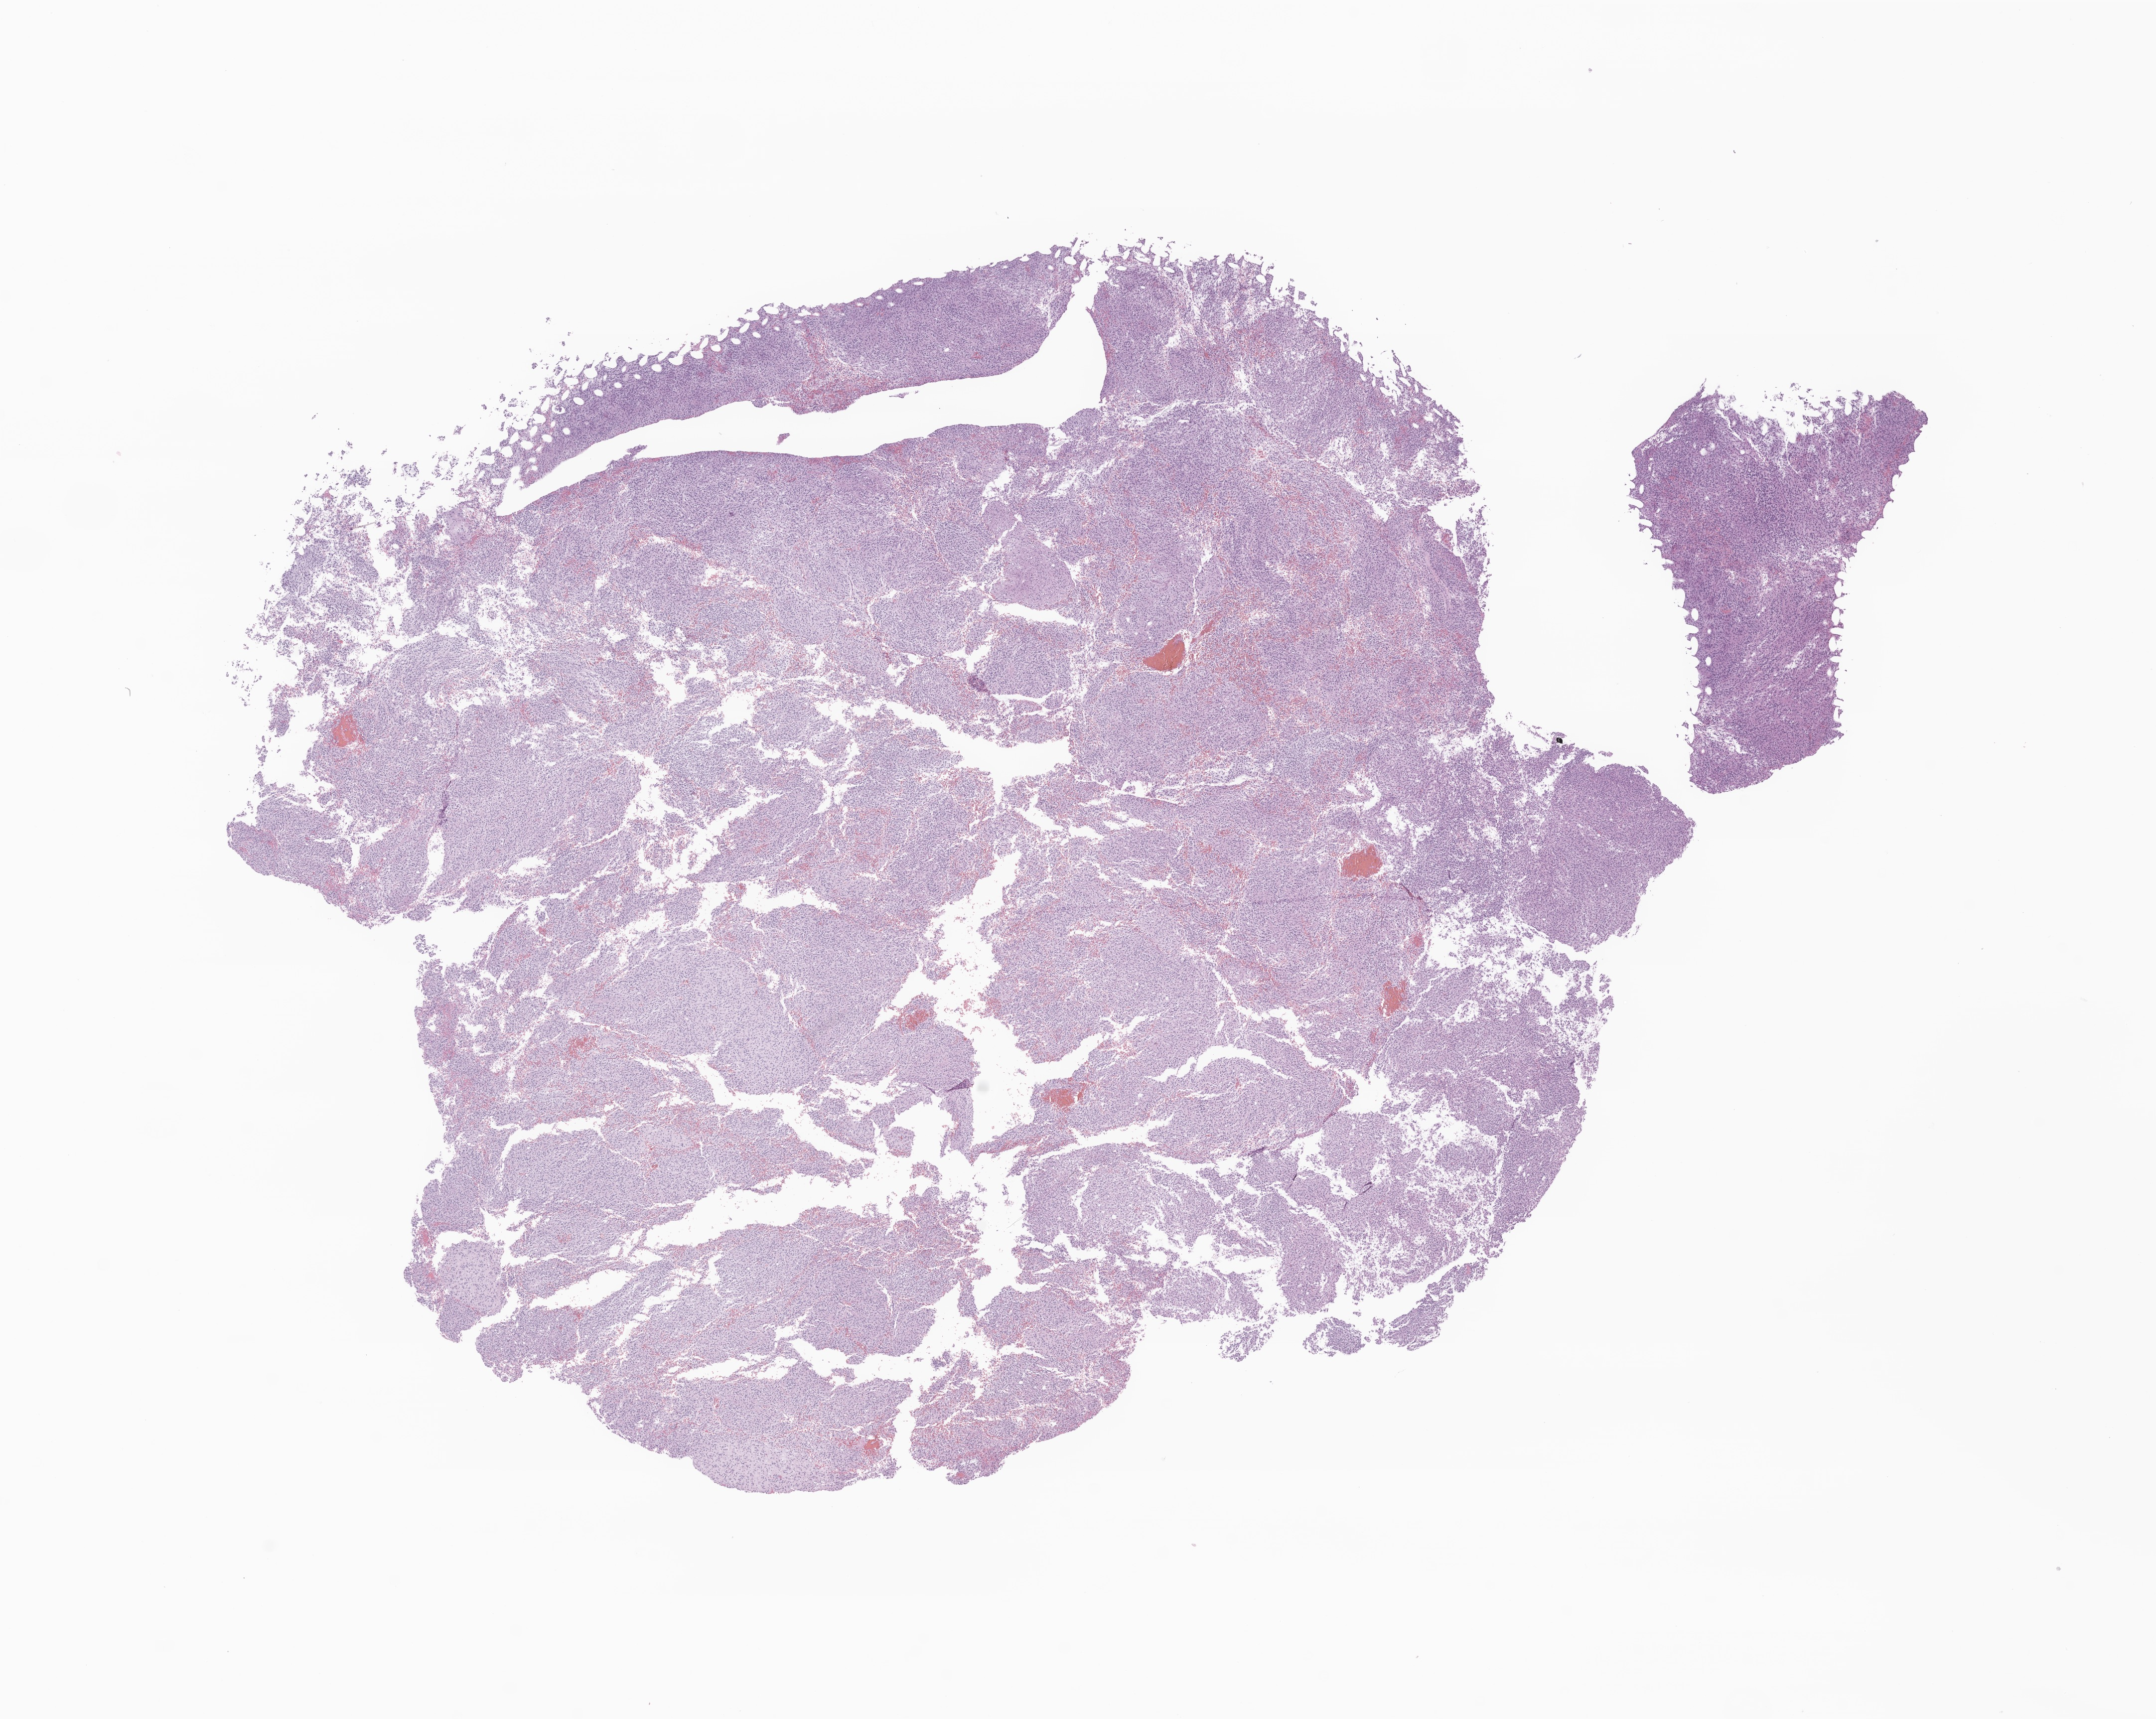
Whole-slide image, hematoxylin and eosin (H&E) stain of tumor tissue from the brain — shown as a low-resolution overview of the whole scanned area (about 18.2 x 14.5 mm), FFPE section. Patient: male, age 124 months (10 years 4 months).
Diagnosis: Glioma, malignant.